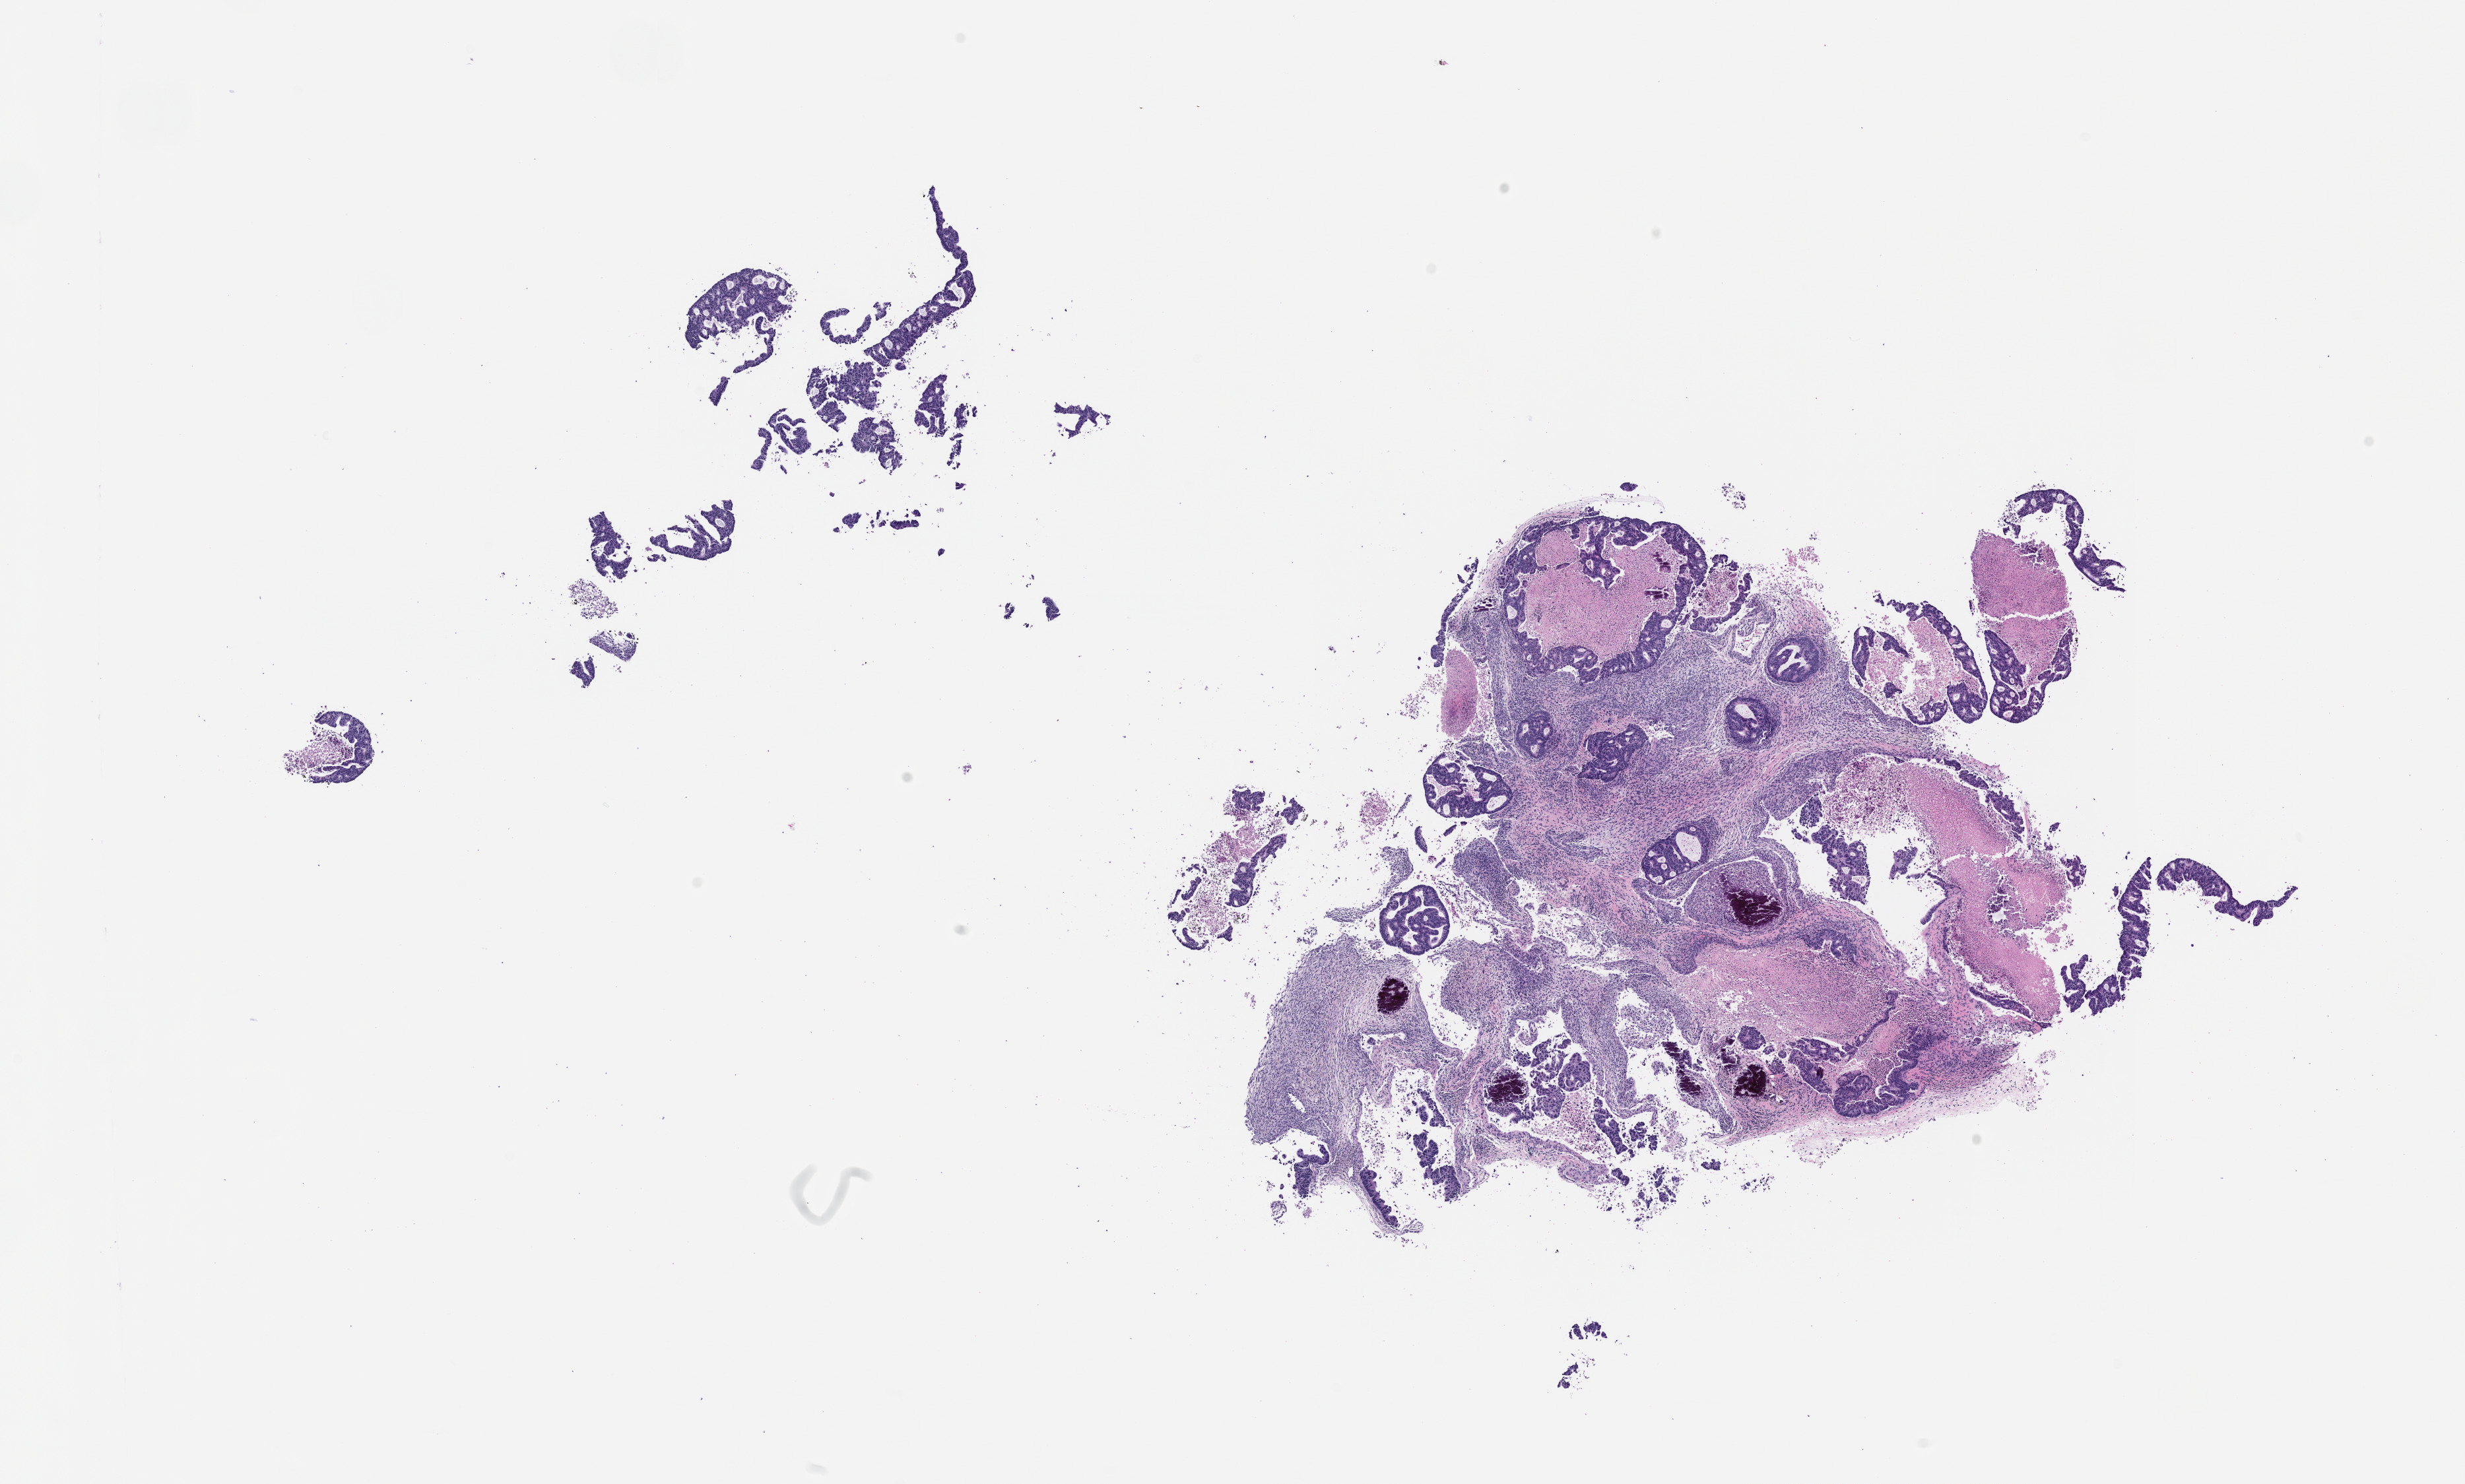
Whole-slide image, haematoxylin and eosin: patient-derived xenograft (human tumor grown in a mouse), passage 1 — low-resolution overview of the scanned area, about 15.0 x 9.0 mm. FFPE section. Originating tumor site category: rectum.
Originating patient diagnosis: Rectal Adenocarcinoma.